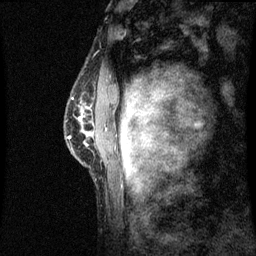
Breast MRI (dynamic contrast-enhanced), one sagittal slice. Slice 47 of 60 in the series (ordered by position). Dynamic contrast-enhanced series, image 2 of 3 at this slice position (ordered by acquisition). 1.5 T. TE 4.2 ms, TR 8.9 ms. 2 mm slice thickness. 256 × 256 image matrix. Female patient, age 50 years. Case-level facts recorded for this patient, not image findings: setting: breast cancer imaged before/during neoadjuvant chemotherapy; receptor status: triple-negative.
Annotated regions visible in this slice (semi-automatically segmented with operator editing):
- analysis volume of interest (the breast-tissue region the enhancement analysis was run in; not a lesion): bounding box [x1, y1, x2, y2] px = [68, 86, 97, 165]
- tumour enhancement mask (voxels above the 70 % enhancement threshold inside the analysis volume of interest): [68, 132, 89, 139]